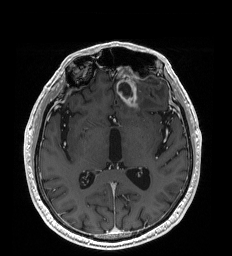
Brain MRI from a brain-tumour surgery series, one axial slice. Slice 105 of 192 in the series (ordered by position). T1-weighted post-contrast. 232 × 256 image matrix. Case-level facts recorded for this patient, not image findings: histopathology: Glioblastoma; WHO grade: 4; IDH mutation: no.
Structures marked on this image (outlined manually by an expert reader):
- tumour: bounding box [x1, y1, x2, y2] px = [118, 84, 137, 107]